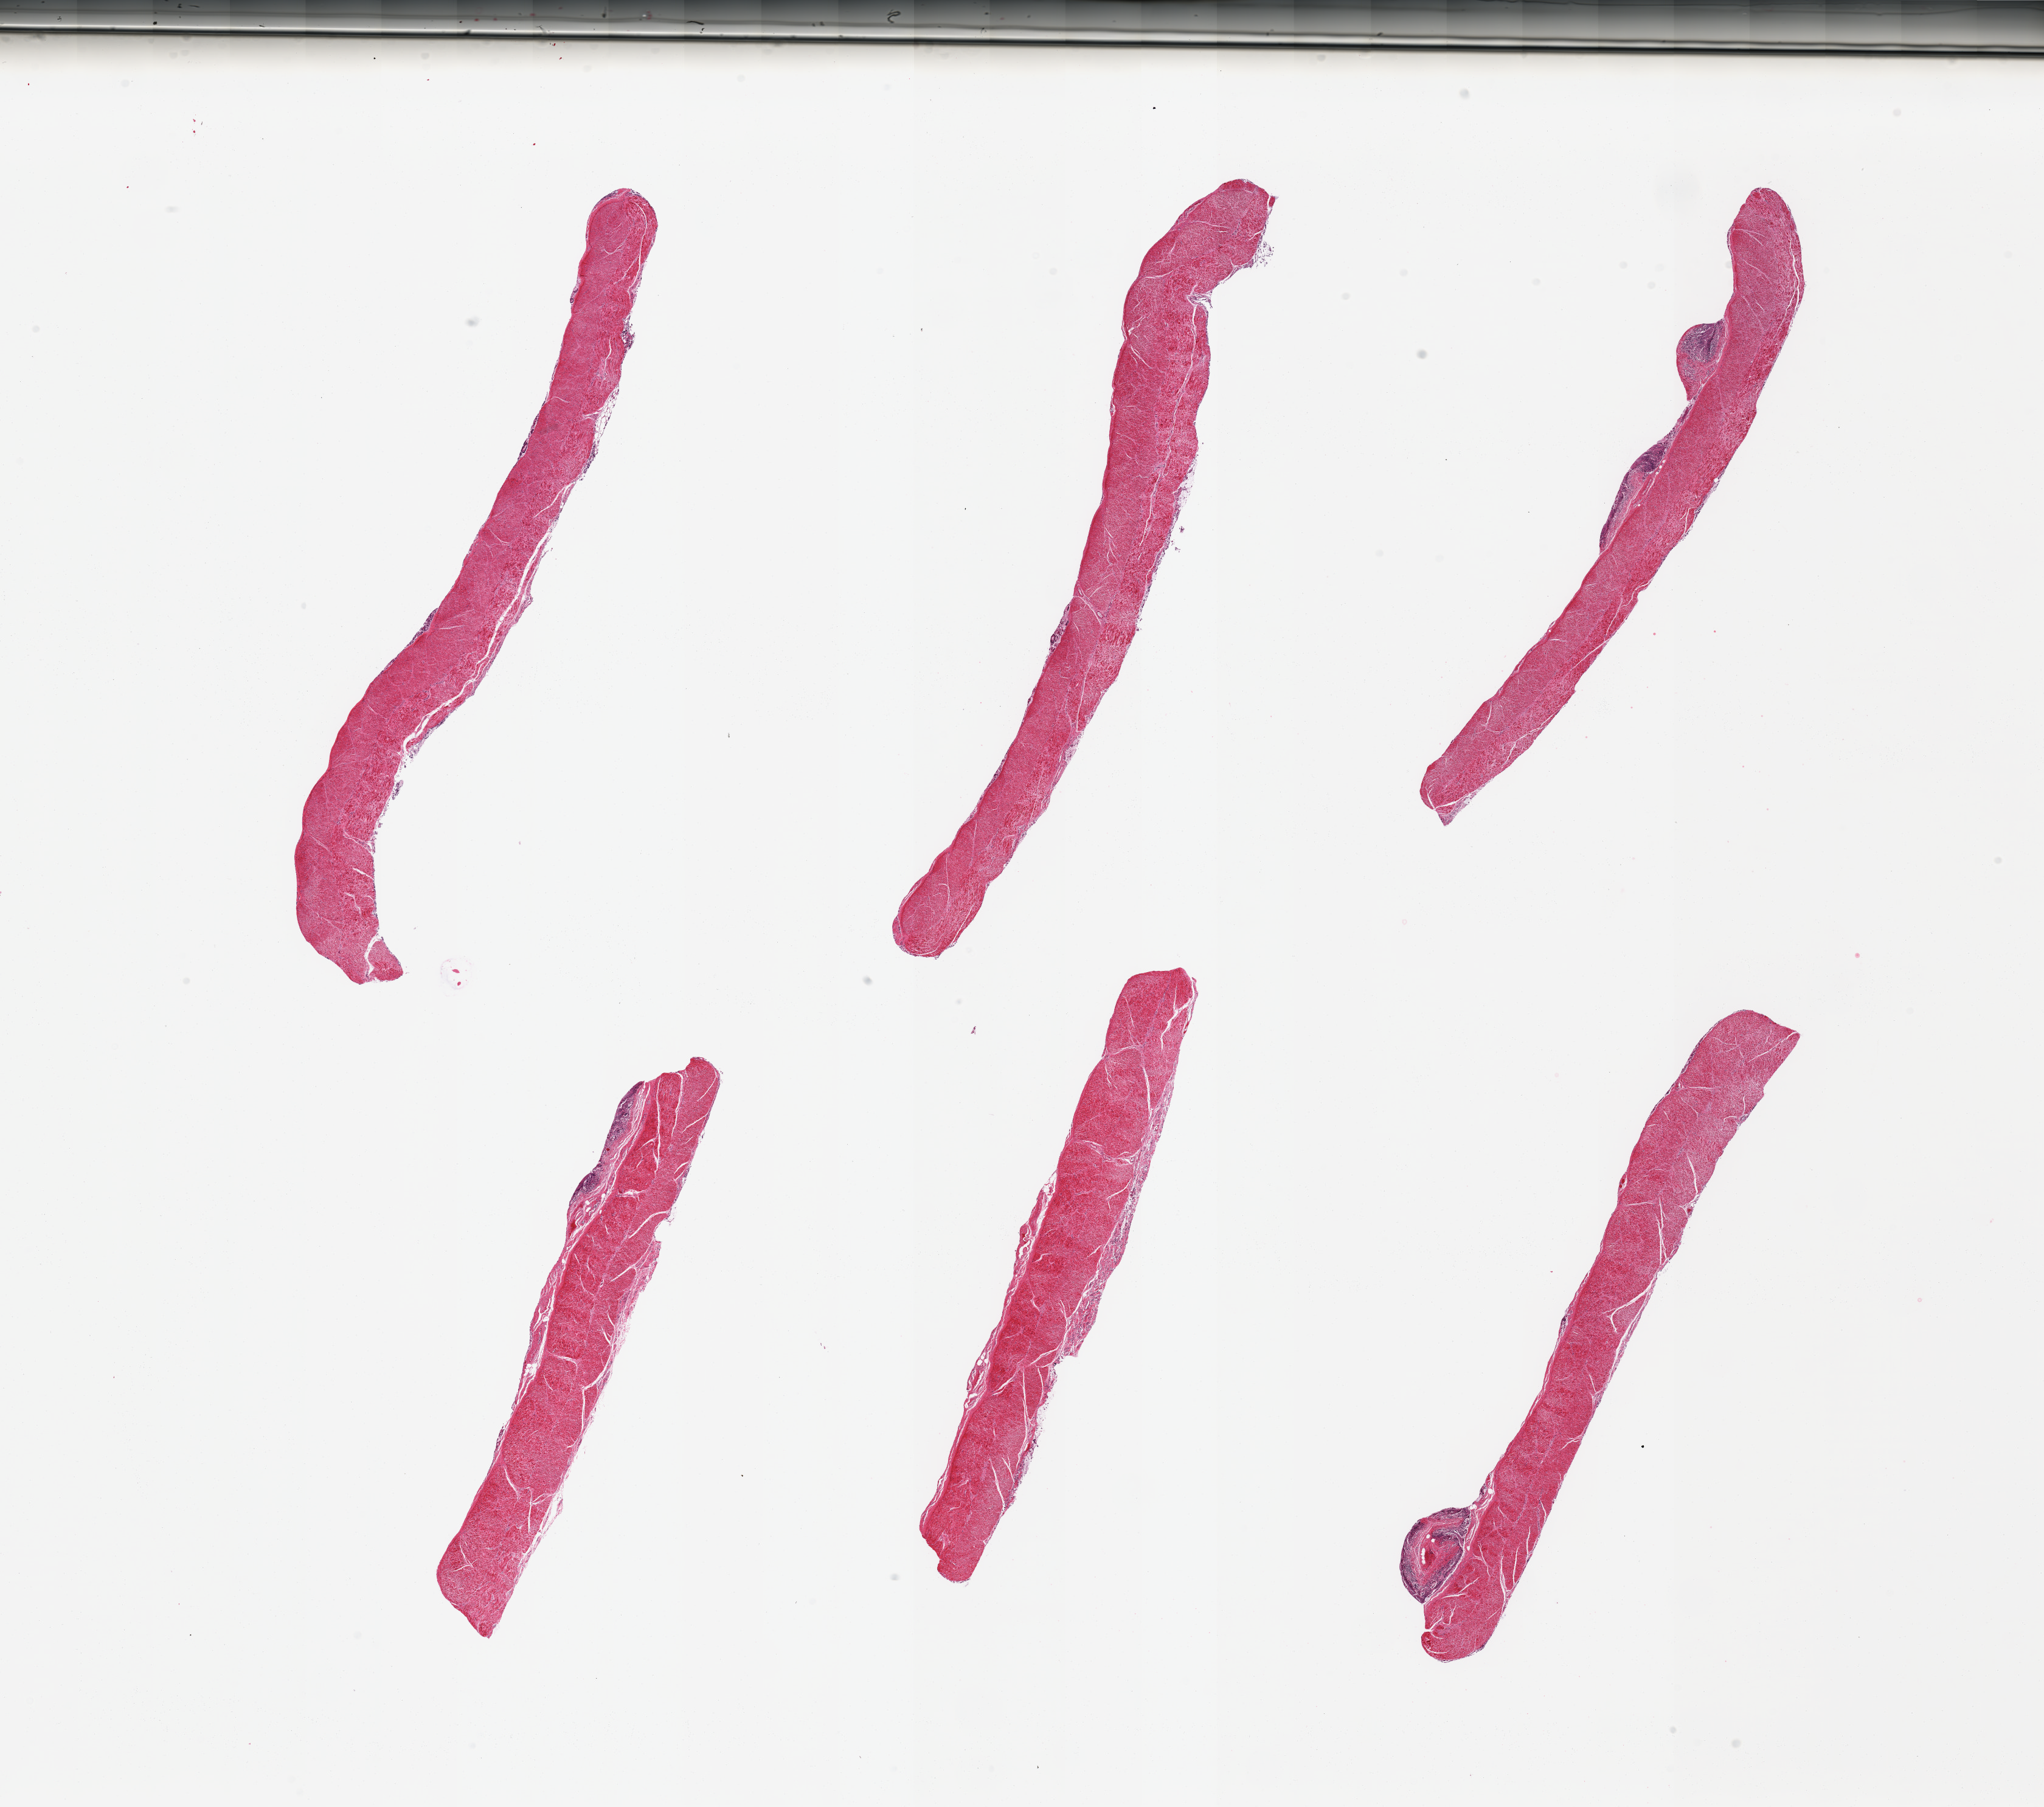
Haematoxylin and eosin whole-slide image — low-resolution overview of the scanned area, about 26.6 x 23.5 mm (acquisition: 20x scan); PAXgene-fixed, paraffin-embedded tissue; section of sigmoid colon (target tissue); tissue donor sample.
* pathologist's review note for this sample: 6 pieces, confirmed target muscularis